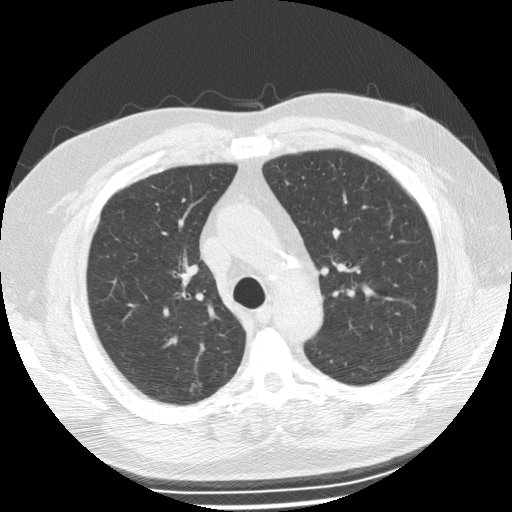
Chest CT (low-dose screening protocol), one axial image. Second screening round (one year after baseline). Lung window (W 1500 / L -600 HU). 2.5 mm slice thickness. Male, age 62 years at enrolment. Former smoker at enrolment.
- Expert-annotated lung lesion, bounding box (x1, y1, x2, y2) in pixels: (176, 371, 215, 410).
- The exam's reader record, not a measurement of the box and not confirmed to be the same lesion: non-calcified nodule or mass ≥4 mm, right upper lobe, 6 × 4 mm, poorly defined margins, ground glass attenuation, pre-existing on the prior screen: yes; interval growth: no.
- Participant outcome: lung cancer diagnosed 405 days after this screen — bronchiolo-alveolar adenocarcinoma, NOS, right upper lobe, well differentiated (G1), stage IA (AJCC 6th edition), 12 mm at pathology.